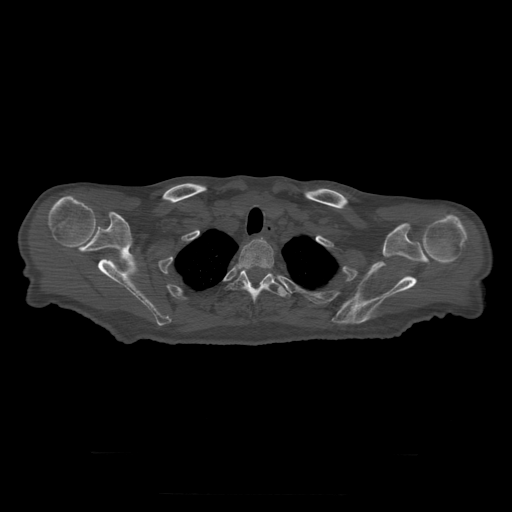
CT including the spine, one axial slice; position 265 of 397 along the scan axis; reconstruction kernel STANDARD; bone window (W 1800 / L 400 HU); 512 × 512 image matrix, field of view 510 × 510 mm. Patient age 73 years. From the clinical record (not read from this slice): primary cancer: prostate.
Outlined on this slice (semi-automatically segmented with operator editing):
- T2 vertebra: bounding box (x1, y1, x2, y2) in pixels: (239, 239, 275, 282)
- T3 vertebra: (226, 270, 290, 304)